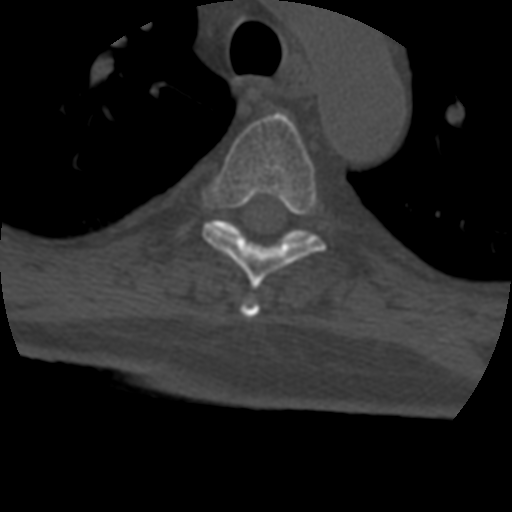
CT including the spine, one axial slice. Slice 317 of 399 in the series (ordered by position). Reconstruction kernel STANDARD. 120 kVp. Bone window (W 1800 / L 400 HU). 1.25 mm slice thickness. 512 × 512 image matrix, field of view 160 × 160 mm. Patient age 69 years. Case-level facts recorded for this patient, not image findings: primary cancer: prostate.
Annotated regions visible in this slice (semi-automatically segmented with operator editing):
- T4 vertebra: bounding box <241,299,260,319> (left, top, right, bottom; pixels)
- T5 vertebra: <203,113,326,290>
- T6 vertebra: <208,220,314,240>